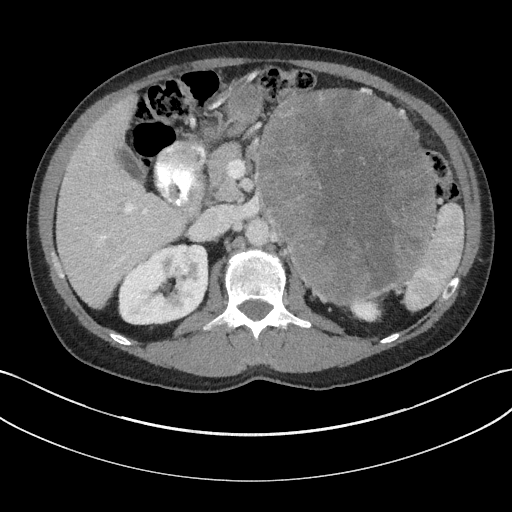
Contrast-enhanced abdominal CT, one axial slice. Slice 106 of 147 in the series (ordered by position). 100 kVp. Soft-tissue window (W 400 / L 40 HU). 3 mm slice thickness. 512 × 512 image matrix, field of view 384 × 384 mm. Patient: male, 58 years. From the clinical record (not read from this slice): diagnosis: adrenocortical carcinoma; tumour side: left adrenal; tumour size at pathology: 22 cm; Ki-67 index: 26 %; stage (as recorded): 2.
Outlined on this slice (semi-automatic segmentation, software-assisted and operator-edited):
- mass: bounding box (x1, y1, x2, y2) in pixels: (259, 90, 435, 301)